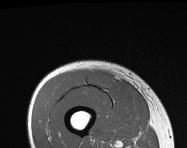
MRI of an extremity soft-tissue mass, one axial slice. Slice 36 of 114 in the series (ordered by position). MR volume resampled by the dataset authors to the PET/CT grid (not the native acquisition matrix). 3.27 mm slice thickness. 187 × 148 image matrix, field of view 183 × 145 mm. Male patient. From the clinical record (not read from this slice): histological type: pleiomorphic leiomyosarcoma; grade: intermediate; site of the primary tumour: right thigh.
Outlined on this slice (expert contour drawn on MRI and transferred to this co-registered scan by the dataset authors):
- gross tumour volume including surrounding oedema: box from (x=88, y=72) to (x=112, y=89) px